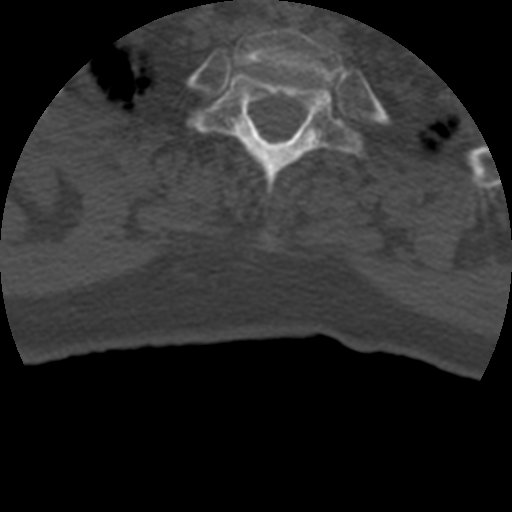
CT including the spine, one axial slice; position 371 of 399 along the scan axis; reconstruction kernel STANDARD; bone window (W 1800 / L 400 HU); 512 × 512 image matrix. Patient age 69 years. Case-level facts recorded for this patient, not image findings: primary cancer: prostate.
Outlined on this slice (semi-automatically segmented with operator editing):
- T1 vertebra: bounding box (x1, y1, x2, y2) in pixels: (235, 29, 342, 94)
- T2 vertebra: (194, 71, 364, 240)